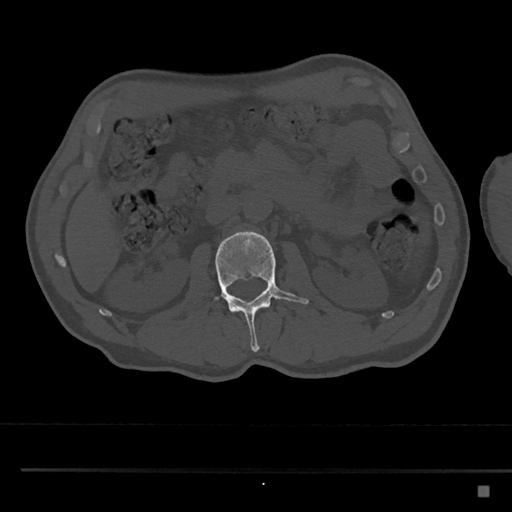
CT including the spine, one axial slice; slice 757 of 797 in the series (ordered by position); reconstruction kernel Br40s/3; bone window (W 1800 / L 400 HU); 0.5 mm slice thickness; 512 × 512 image matrix, field of view 391 × 391 mm. Patient: male, 59 years. From the clinical record (not read from this slice): primary cancer: prostate.
Outlined on this slice (semi-automatically segmented with operator editing):
- L2 vertebra: bounding box [x1, y1, x2, y2] px = [215, 230, 309, 352]